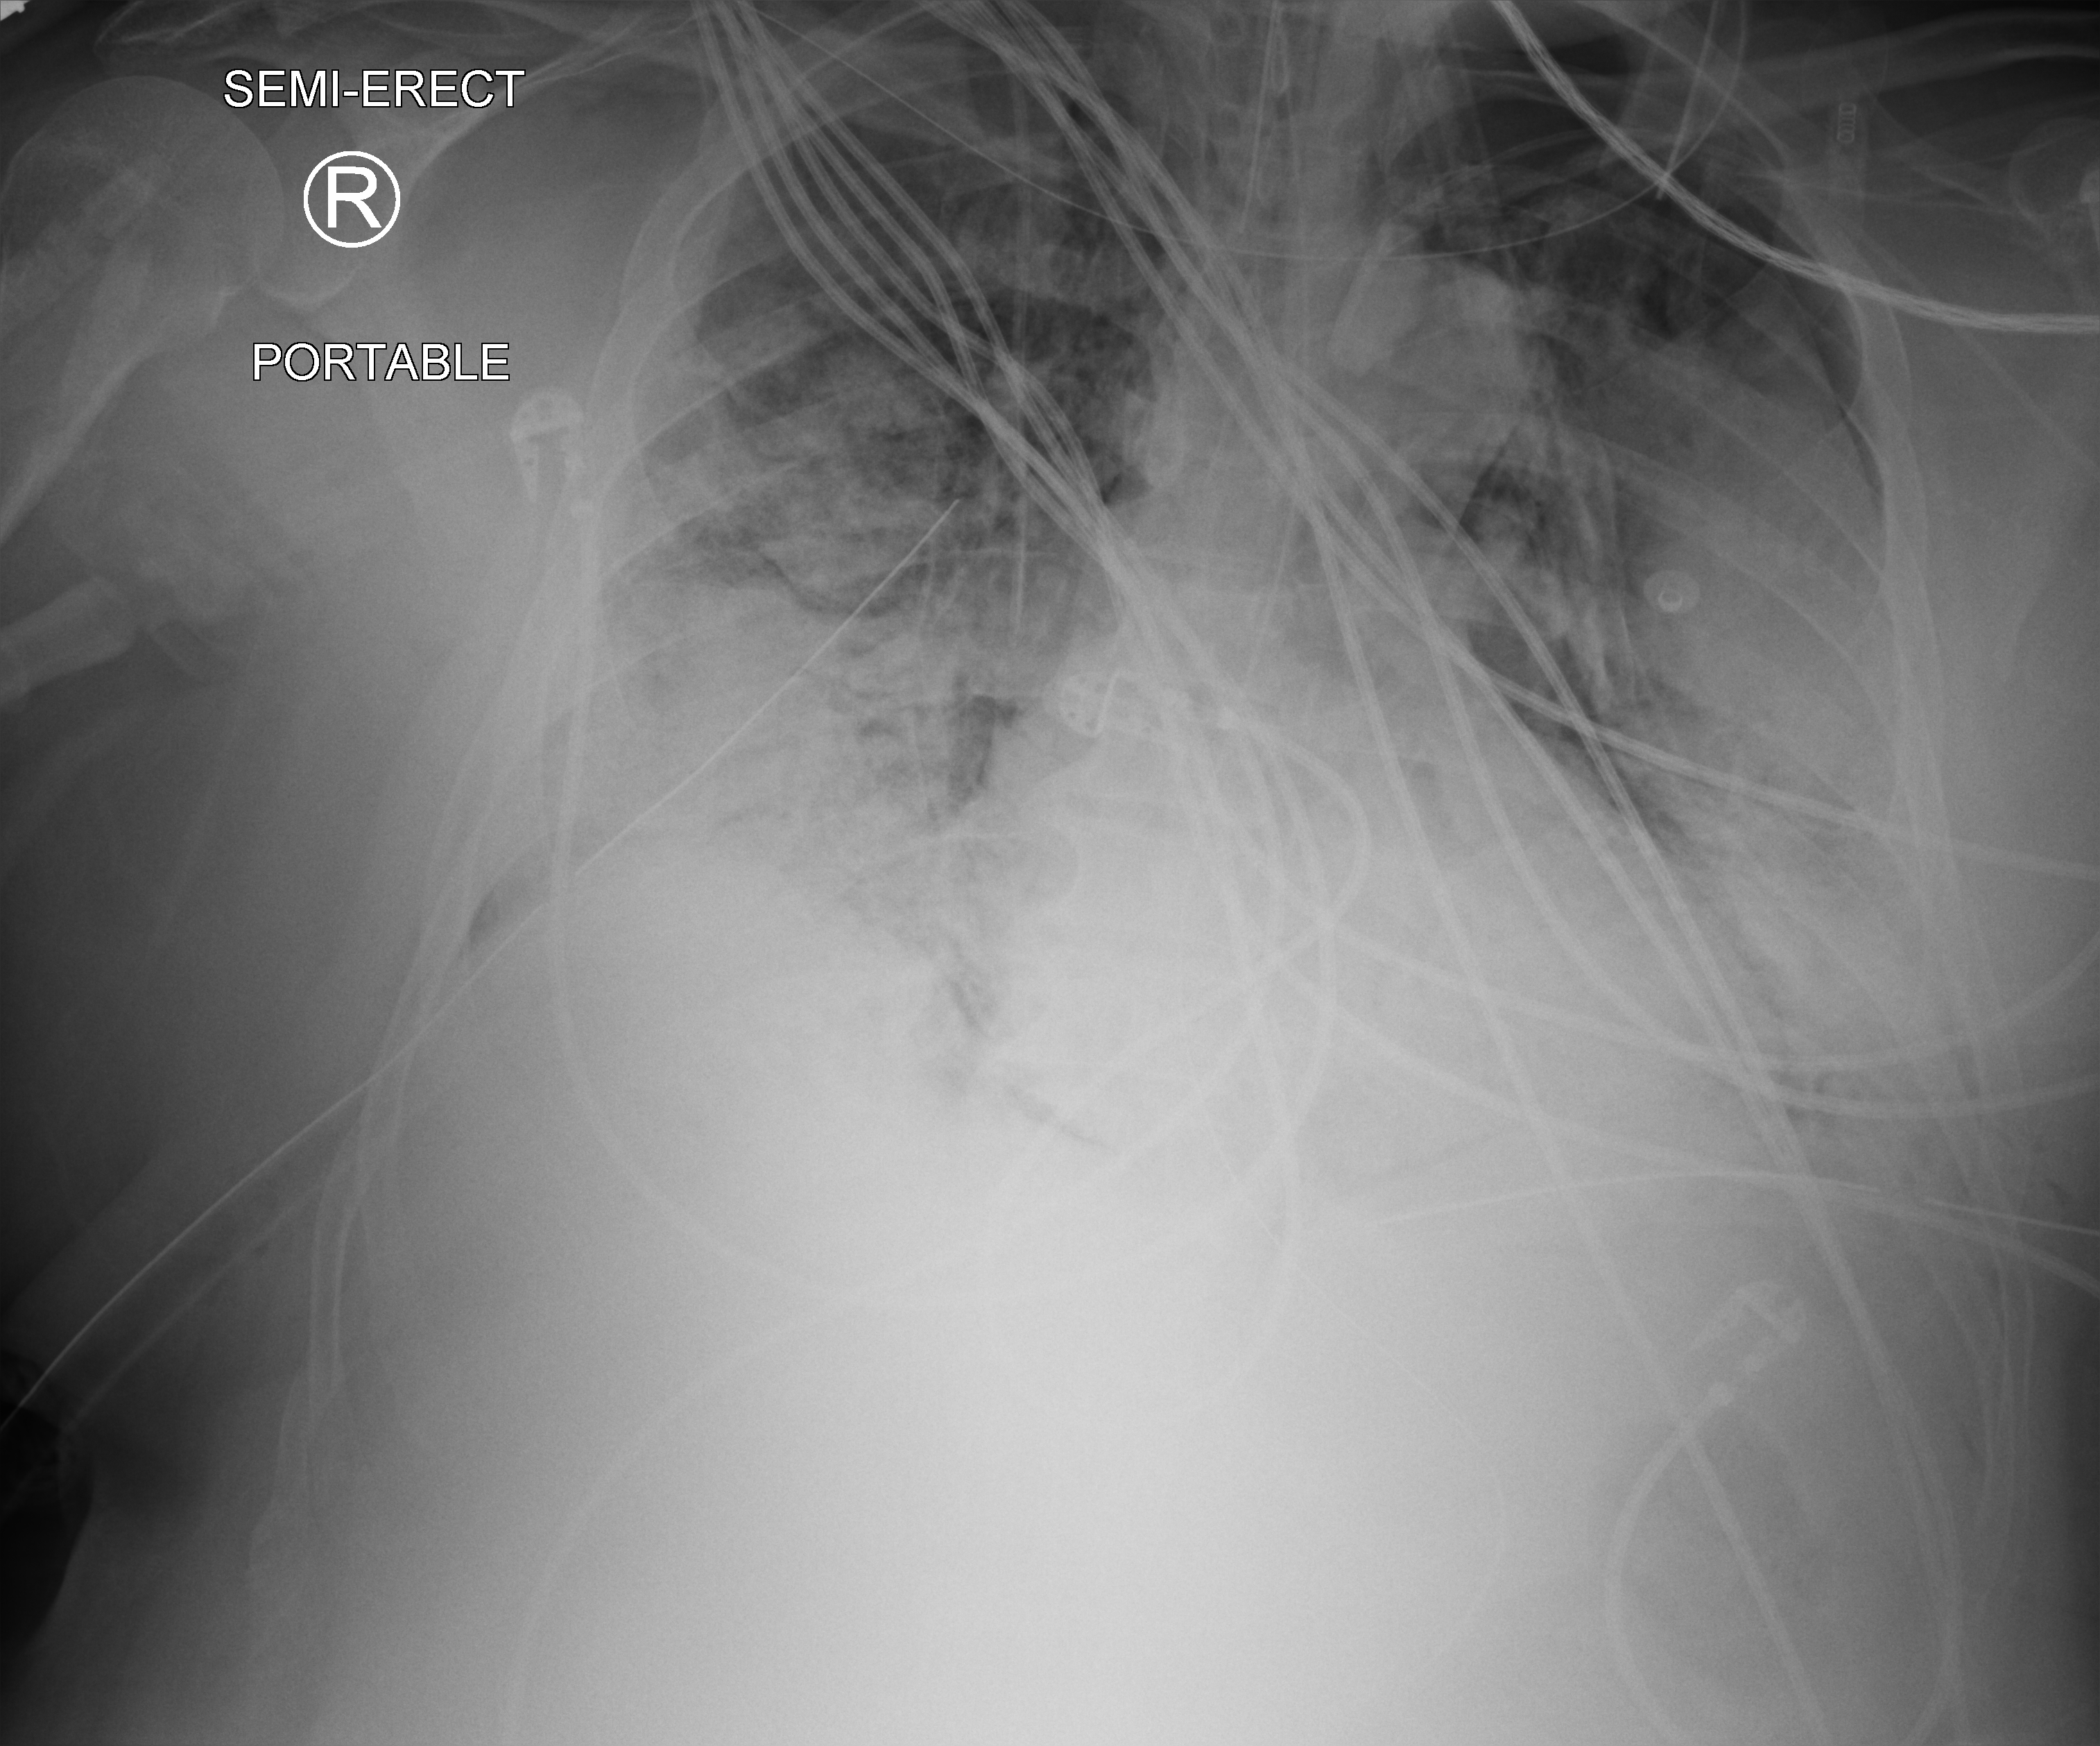
Chest X-ray (portable), anteroposterior (AP) projection. Adult patient hospitalised with COVID-19, age 18–59 years.
Hospital-stay facts (about this admission, not read from this image; timing relative to this image not recorded): COPD (admission record): no; admitted to intensive care during this hospital stay: yes; mechanically ventilated during this hospital stay: yes.